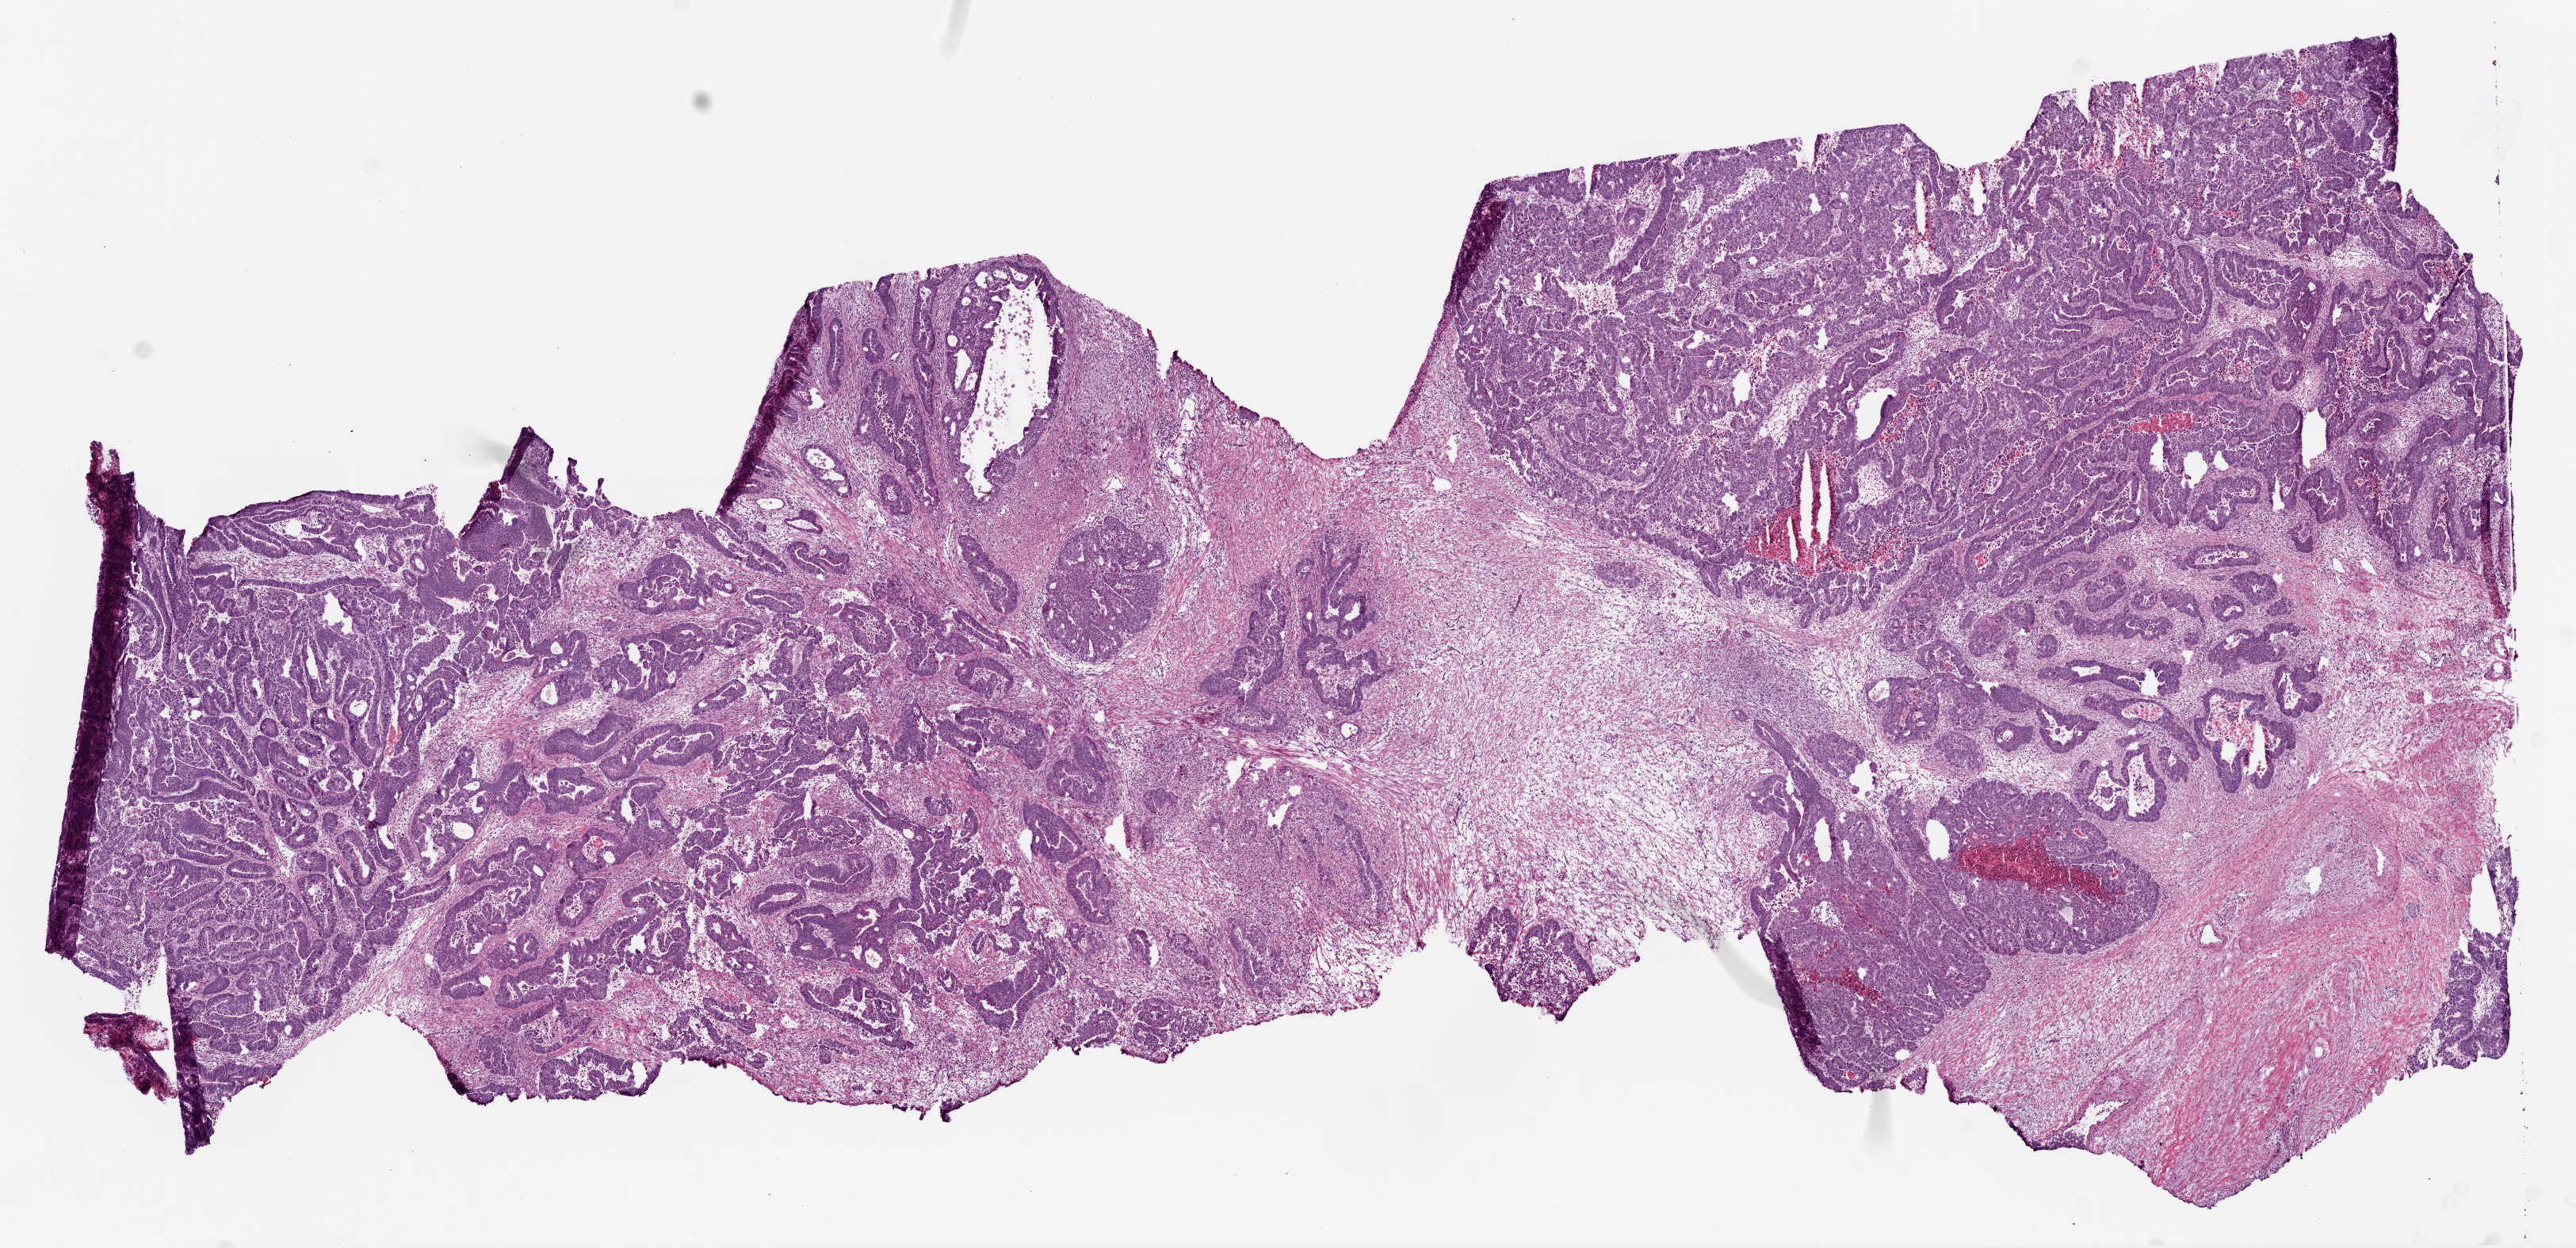
Digitized H&E-stained tissue section (whole slide), low-resolution overview of the scanned area, about 13.0 x 6.3 mm (slide scanned at 20x); frozen section from the top of the tissue portion; sample: primary tumour, colon. Patient: male, age at initial diagnosis 73 years. Composition of this section per pathologist review: tumour cells 80%, tumour nuclei 80%, normal cells 6%, stromal cells 11%, necrosis 3%. Infiltration values recorded for this section: lymphocyte infiltration 5%, monocyte infiltration 1%, neutrophil infiltration 5%.
Lymph nodes positive (case pathology): 11 of 23 examined. AJCC pathologic stage: IIIC. Diagnosis: Adenocarcinoma, NOS (ascending colon).